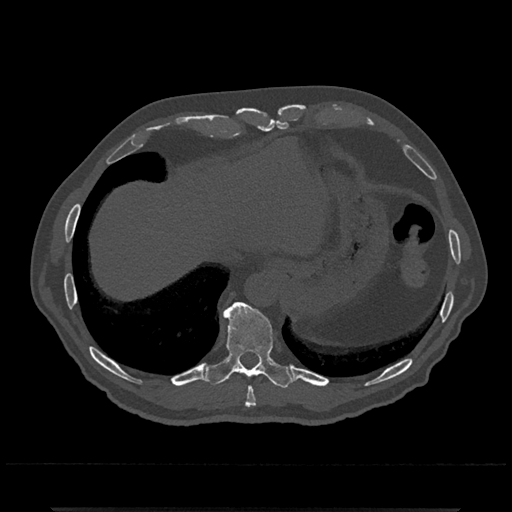
CT including the spine, one axial slice. Slice 565 of 797 in the series (ordered by position). 120 kVp. Bone window (W 1800 / L 400 HU). 0.5 mm slice thickness. 512 × 512 image matrix, field of view 393 × 393 mm. Patient: male, 67 years. Case-level facts recorded for this patient, not image findings: primary cancer: prostate.
Outlined on this slice (semi-automatic segmentation, software-assisted and operator-edited):
- T10 vertebra: bounding box [x1, y1, x2, y2] px = [204, 301, 292, 389]
- T9 vertebra: [245, 387, 256, 407]